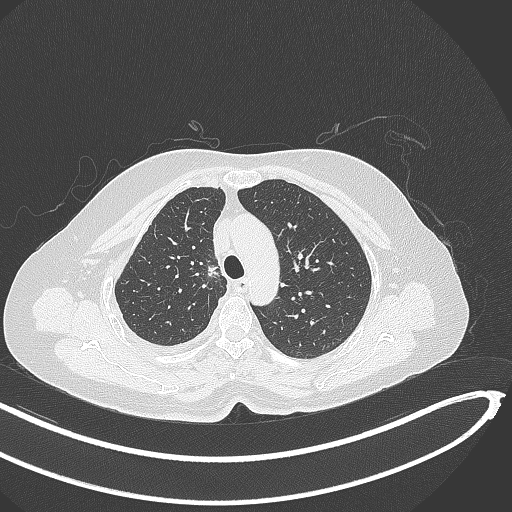
Chest CT, one axial slice; slice 281 of 345 in the series (ordered by position); reconstruction kernel B70f; 120 kVp; lung window (W 1500 / L -600 HU); 1 mm slice thickness; 512 × 512 image matrix, field of view 400 × 400 mm. Patient: female, 64 years. Case-level facts recorded for this patient, not image findings: clinical TNM (as recorded): T1b N0 M1.
Outlined on this slice (bounding box drawn by a radiologist):
- lung tumour (recorded histology: adenocarcinoma): bounding box (x1, y1, x2, y2) in pixels: (205, 258, 225, 281)